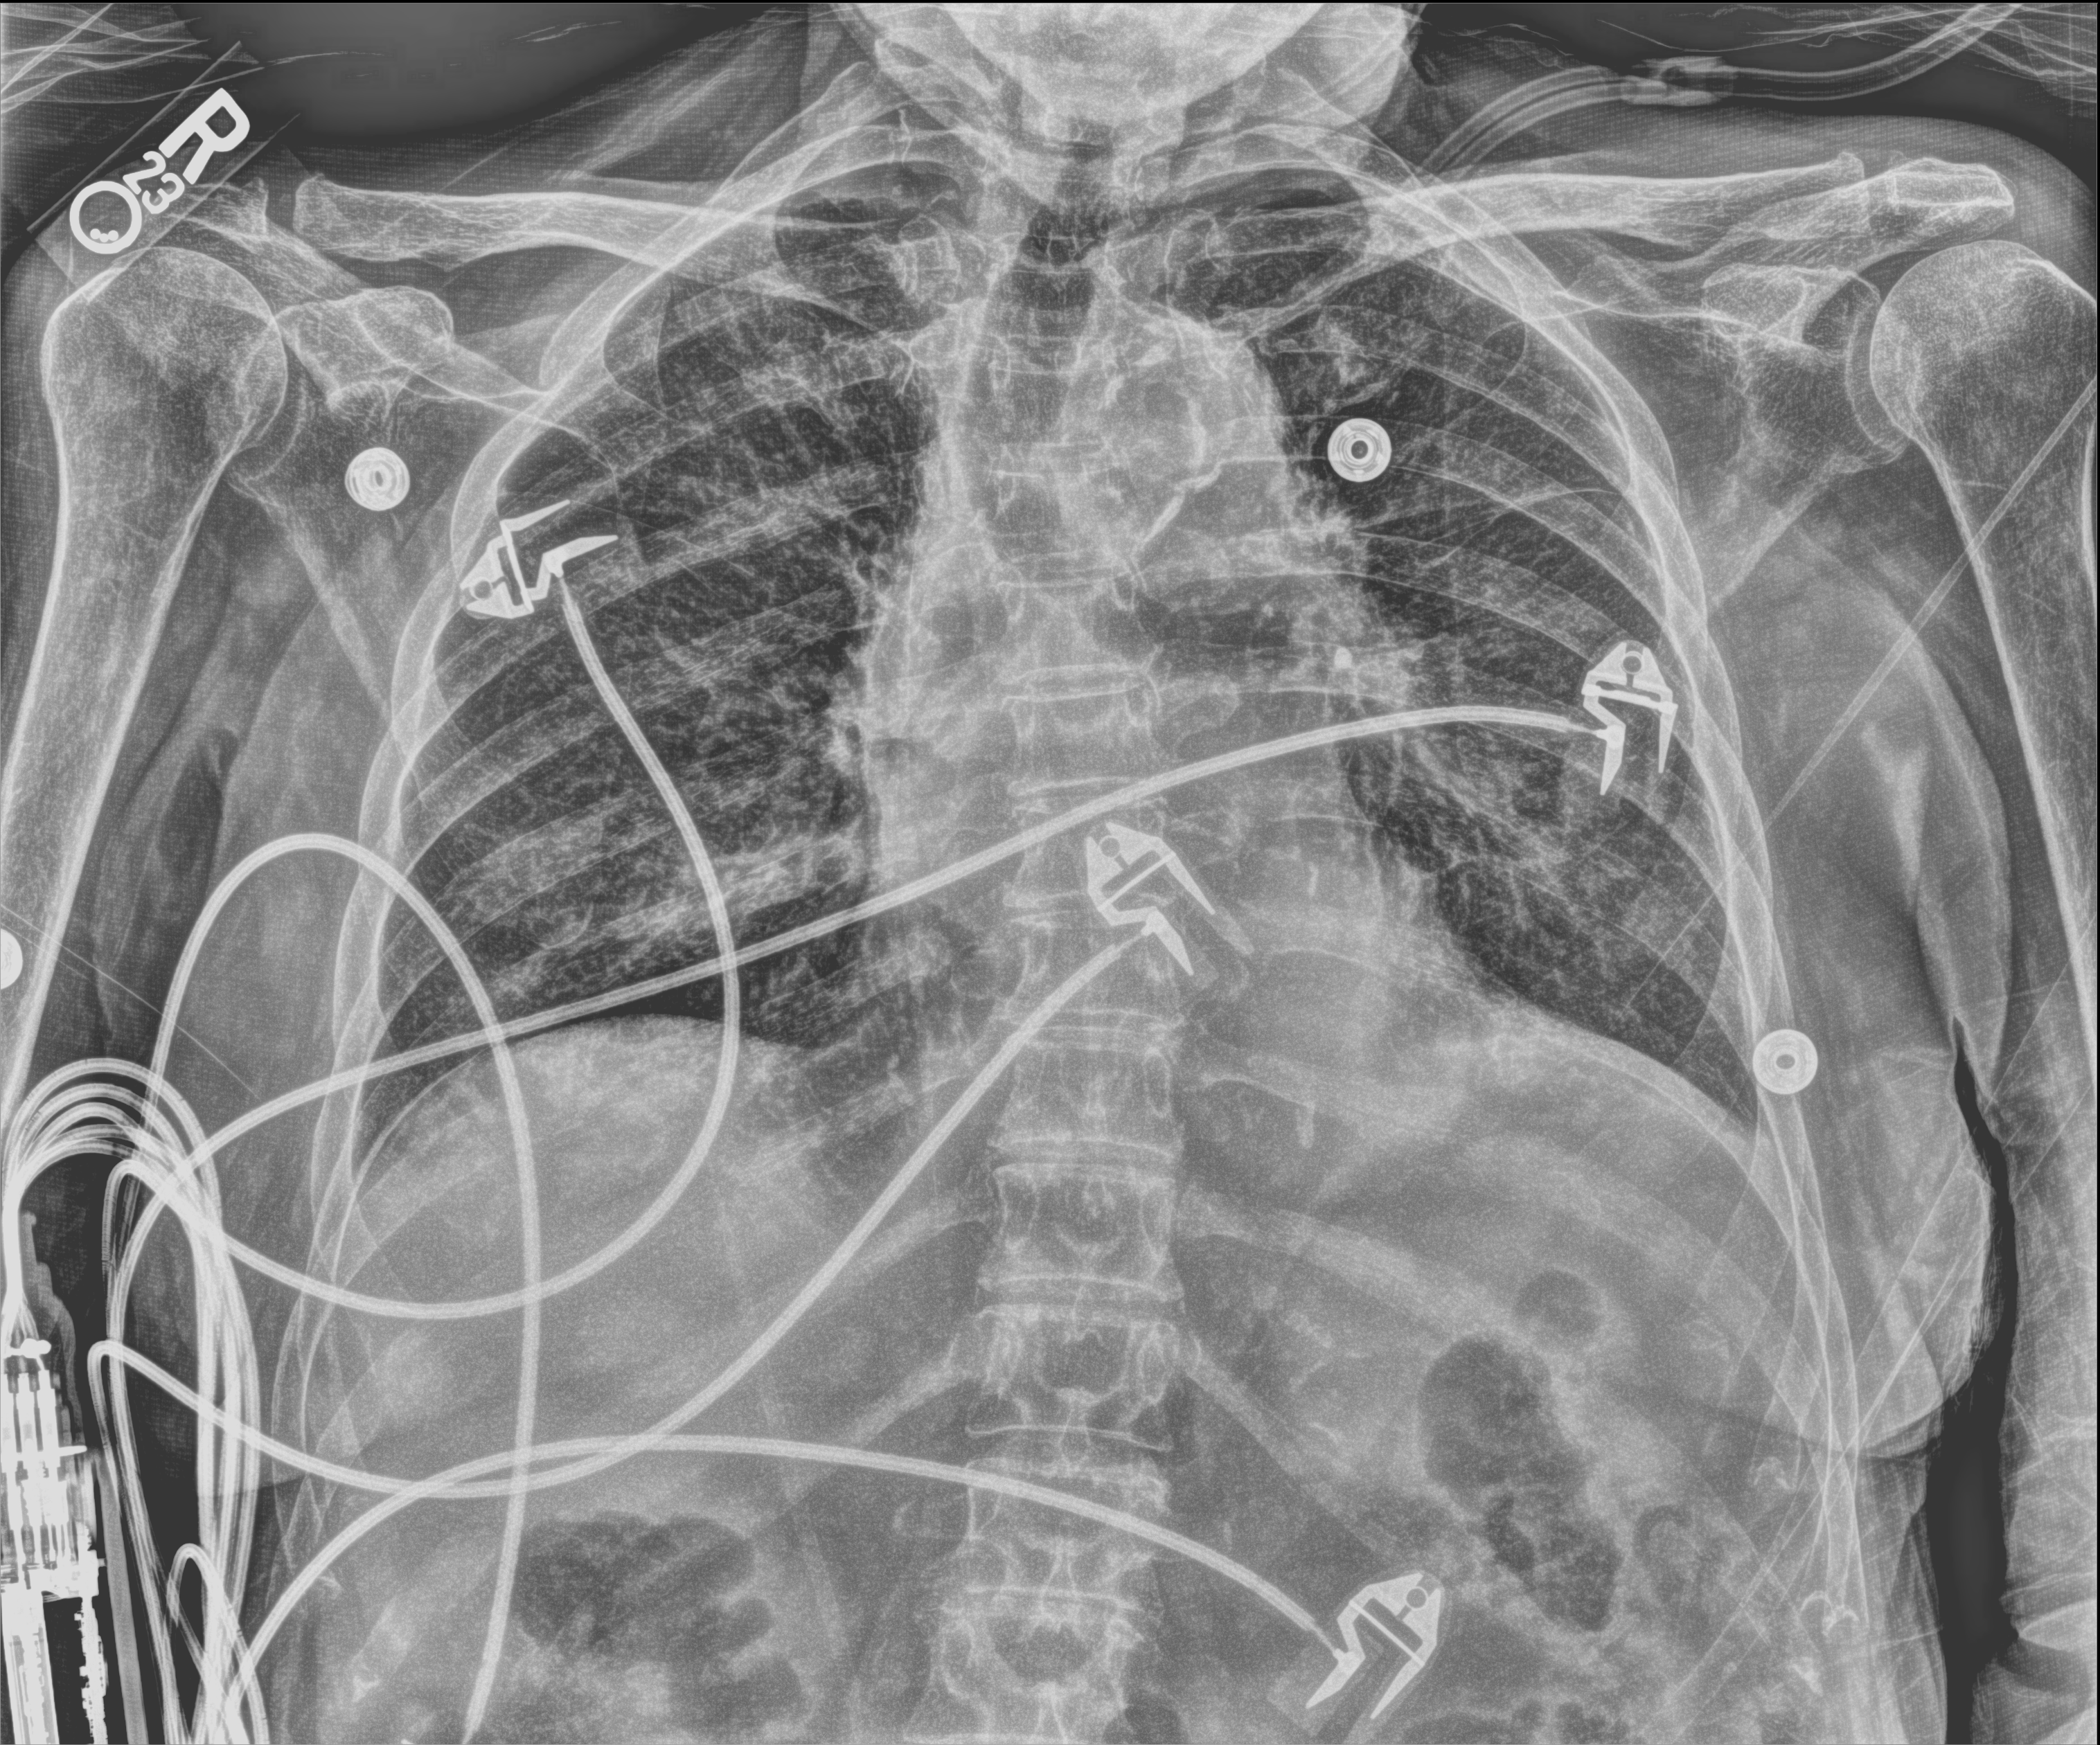
Chest X-ray (portable); anteroposterior (AP) projection. Patient hospitalised with COVID-19; female, aged 75–90 years.
Hospital-stay facts (about this admission, not read from this image; timing relative to this image not recorded): length of hospital stay: 8 days; mechanically ventilated during this hospital stay: no; smoking status (admission record): never.